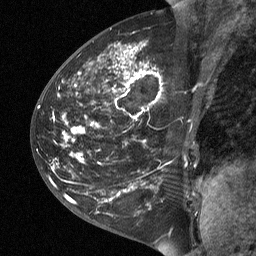
Breast MRI (dynamic contrast-enhanced), one sagittal slice. Slice 26 of 64 in the series (ordered by position). Dynamic contrast-enhanced study with each time point stored as its own series, time point 2 of 3 at this slice position (early post-contrast, ordered by acquisition time). 1.5 T. TE 4.8 ms, TR 27 ms. 2 mm slice thickness. 256 × 256 image matrix, field of view 200 × 200 mm. Patient: female, 42 years. Case-level facts recorded for this patient, not image findings: setting: breast cancer imaged before/during neoadjuvant chemotherapy; receptor status: triple-negative.
Outlined on this slice (semi-automatic segmentation, software-assisted and operator-edited):
- analysis volume of interest (the breast-tissue region the enhancement analysis was run in; not a lesion): bounding box <43,29,203,190> (left, top, right, bottom; pixels)
- tumour enhancement mask (voxels above the 90 % enhancement threshold inside the analysis volume of interest): <66,48,150,190>